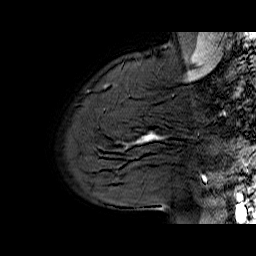
Breast MRI (dynamic contrast-enhanced), one sagittal slice. Slice 52 of 70 in the series (ordered by position). Dynamic contrast-enhanced series, time point 2 of 6 at this slice position (early post-contrast). 1.5 T. TE 6.5 ms, TR 33 ms. 4 mm slice thickness. 256 × 256 image matrix, field of view 200 × 200 mm. Female patient. From the clinical record (not read from this slice): setting: breast cancer imaged before/during neoadjuvant chemotherapy; receptor status: HER2-positive.
Outlined on this slice (semi-automatic segmentation, software-assisted and operator-edited):
- analysis volume of interest (the breast-tissue region the enhancement analysis was run in; not a lesion): bounding box (x1, y1, x2, y2) in pixels: (113, 112, 174, 170)
- tumour enhancement mask (voxels above the 100 % enhancement threshold inside the analysis volume of interest): (138, 132, 157, 141)